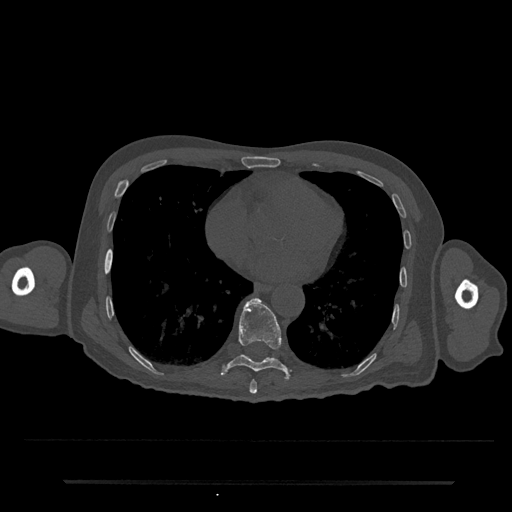
CT including the spine, one axial slice; 120 kVp; bone window (W 1800 / L 400 HU); 0.5 mm slice thickness; 512 × 512 image matrix, field of view 427 × 427 mm. Patient: male, 74 years. Case-level facts recorded for this patient, not image findings: primary cancer: prostate.
Outlined on this slice (semi-automatic segmentation, software-assisted and operator-edited):
- T8 vertebra: bounding box [x1, y1, x2, y2] px = [249, 380, 257, 394]
- T9 vertebra: [221, 298, 291, 379]